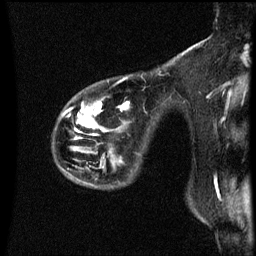
Breast MRI (dynamic contrast-enhanced), one sagittal slice; position 45 of 60 along the scan axis; dynamic contrast-enhanced series, image 2 of 3 at this slice position (ordered by acquisition); 1.5 T; TE 4.2 ms, TR 8.9 ms; 2 mm slice thickness; 256 × 256 image matrix, field of view 200 × 200 mm. Female patient, age 44 years. From the clinical record (not read from this slice): setting: breast cancer imaged before/during neoadjuvant chemotherapy; receptor status: HR-positive, HER2-negative.
Annotated regions visible in this slice (semi-automatic segmentation, software-assisted and operator-edited):
- analysis volume of interest (the breast-tissue region the enhancement analysis was run in; not a lesion): bounding box [x1, y1, x2, y2] px = [55, 78, 130, 187]
- tumour enhancement mask (voxels above the 70 % enhancement threshold inside the analysis volume of interest): [89, 102, 129, 129]